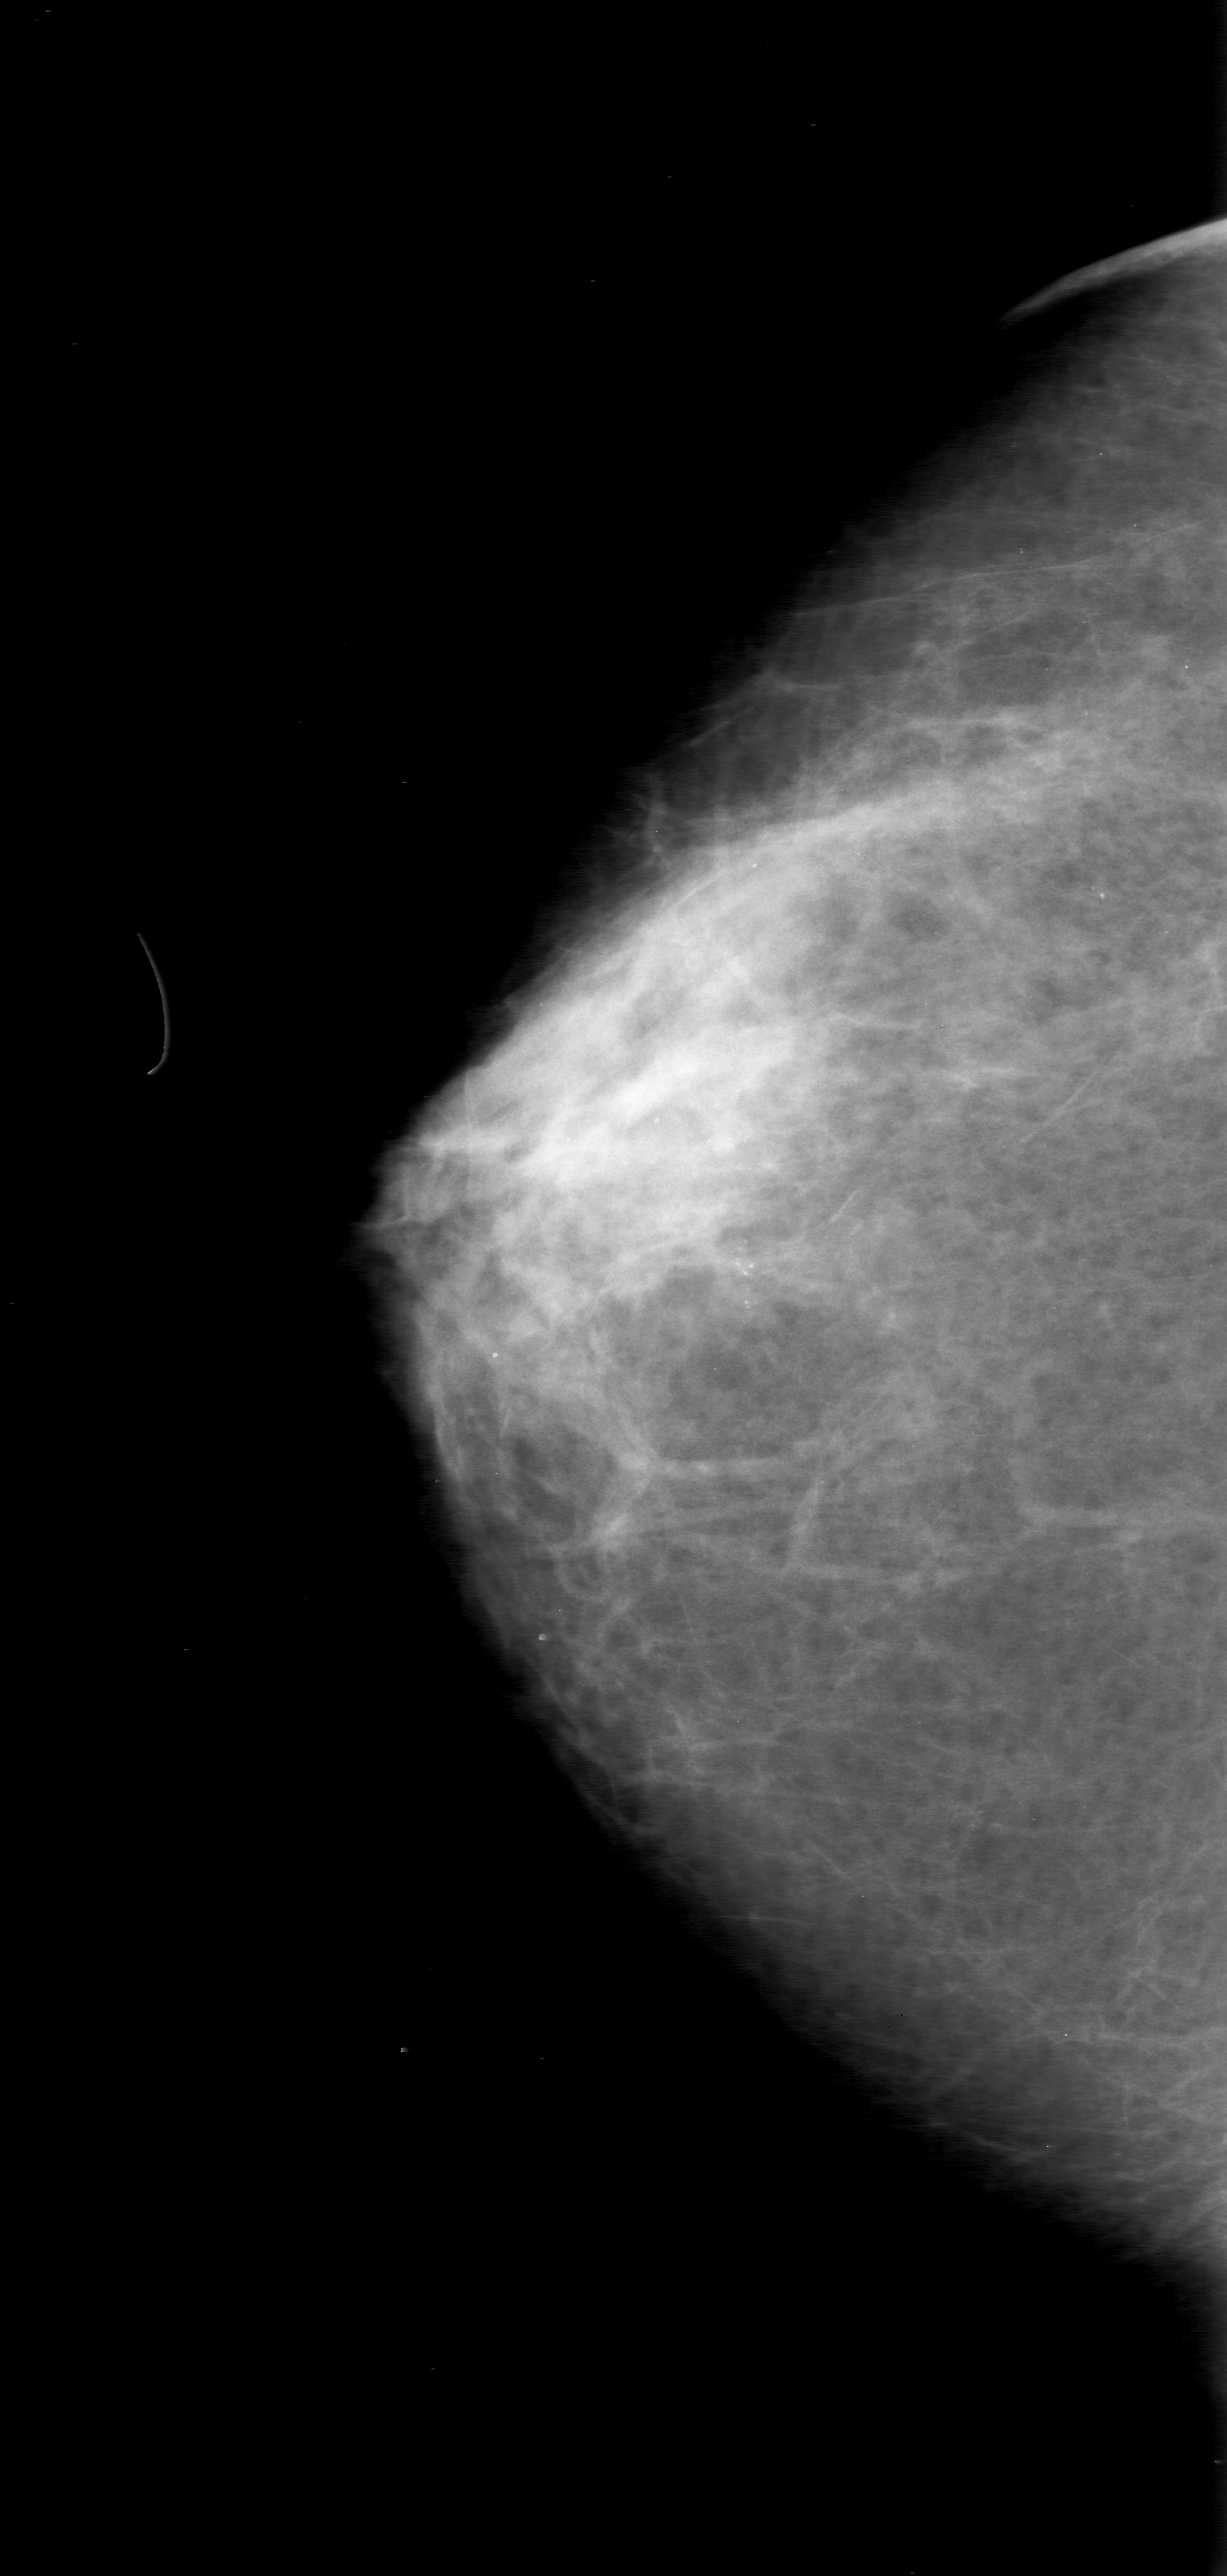
Scanned film-screen mammogram; right breast; craniocaudal (CC) view; breast composition: scattered fibroglandular densities (BI-RADS density category 2 of 4).
Radiologist-marked abnormalities on this image: calcifications, morphology pleomorphic, distribution clustered; BI-RADS assessment category 0; subtlety rating 4 on a 1 (subtle) to 5 (obvious) scale; pathology result (as recorded, not read from the image): malignant.